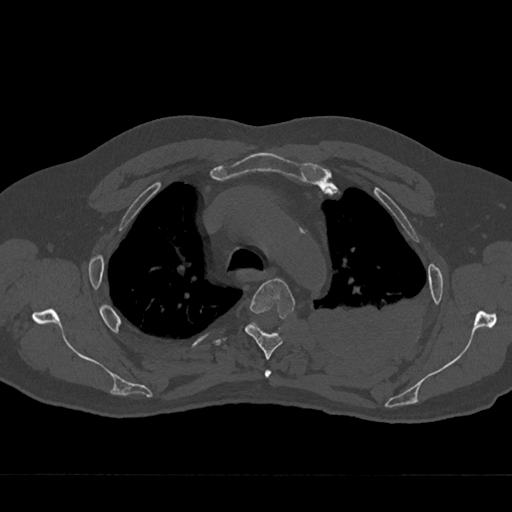
CT including the spine, one axial slice. Slice 518 of 797 in the series (ordered by position). Reconstruction kernel Br40s/3. Bone window (W 1800 / L 400 HU). 512 × 512 image matrix. Male patient, age 75 years. From the clinical record (not read from this slice): primary cancer: renal; vertebrae with lytic lesions (as recorded): T4.
Outlined on this slice (semi-automatic segmentation, software-assisted and operator-edited):
- T3 vertebra: box from (x=264, y=370) to (x=272, y=378) px
- T4 vertebra: (x=245, y=278)–(x=295, y=360)
- T5 vertebra: (x=251, y=323)–(x=258, y=327)